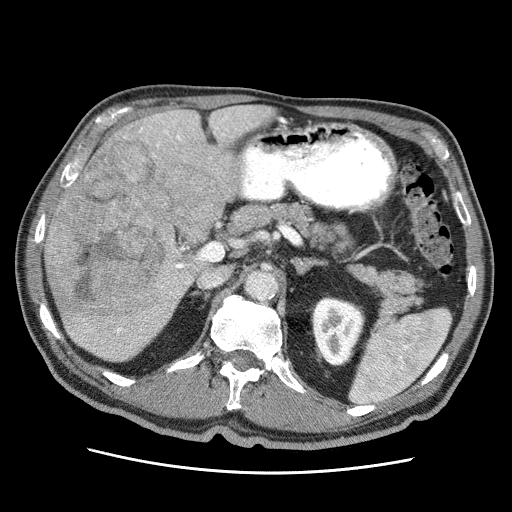
Contrast-enhanced abdominal CT (liver protocol), one axial slice; reconstruction kernel STANDARD; 120 kVp; soft-tissue window (W 400 / L 40 HU); 2.5 mm slice thickness; 512 × 512 image matrix, field of view 360 × 360 mm. From the clinical record (not read from this slice): diagnosis: hepatocellular carcinoma (patient treated with transarterial chemoembolisation; whether this scan precedes or follows treatment is not stated here); TNM stage (as recorded): Stage-IIIA; Child-Pugh class: A; tumour differentiation: well differentiated; tumour nodularity: multinodular.
Annotated regions visible in this slice (semi-automatically segmented with operator editing):
- liver parenchyma outside the tumour (the mass and vessels are separate outlines, so this box may not span the whole liver): bounding box [x1, y1, x2, y2] px = [44, 106, 274, 361]
- mass: [47, 138, 224, 324]
- liver vessels: [90, 114, 248, 348]